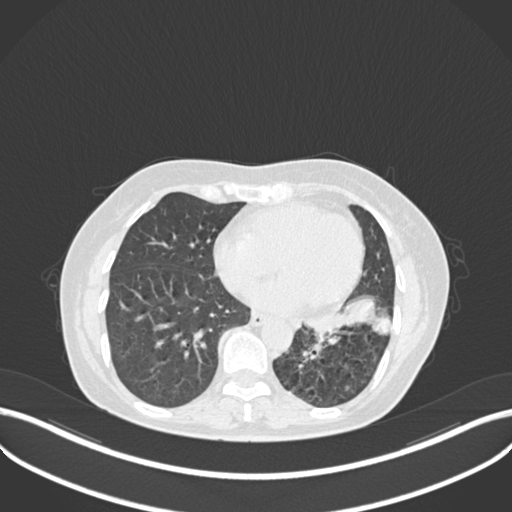
Chest CT, one axial slice. Slice 97 of 270 in the series (ordered by position). 120 kVp. Lung window (W 1500 / L -600 HU). 1 mm slice thickness. 512 × 512 image matrix. Patient: female, 63 years. From the clinical record (not read from this slice): clinical TNM (as recorded): T1b N0 M0; histopathological grade: G2-3.
Annotated regions visible in this slice (rectangle marked by the reading radiologist):
- lung tumour (recorded histology: adenocarcinoma): box from (x=308, y=293) to (x=390, y=341) px